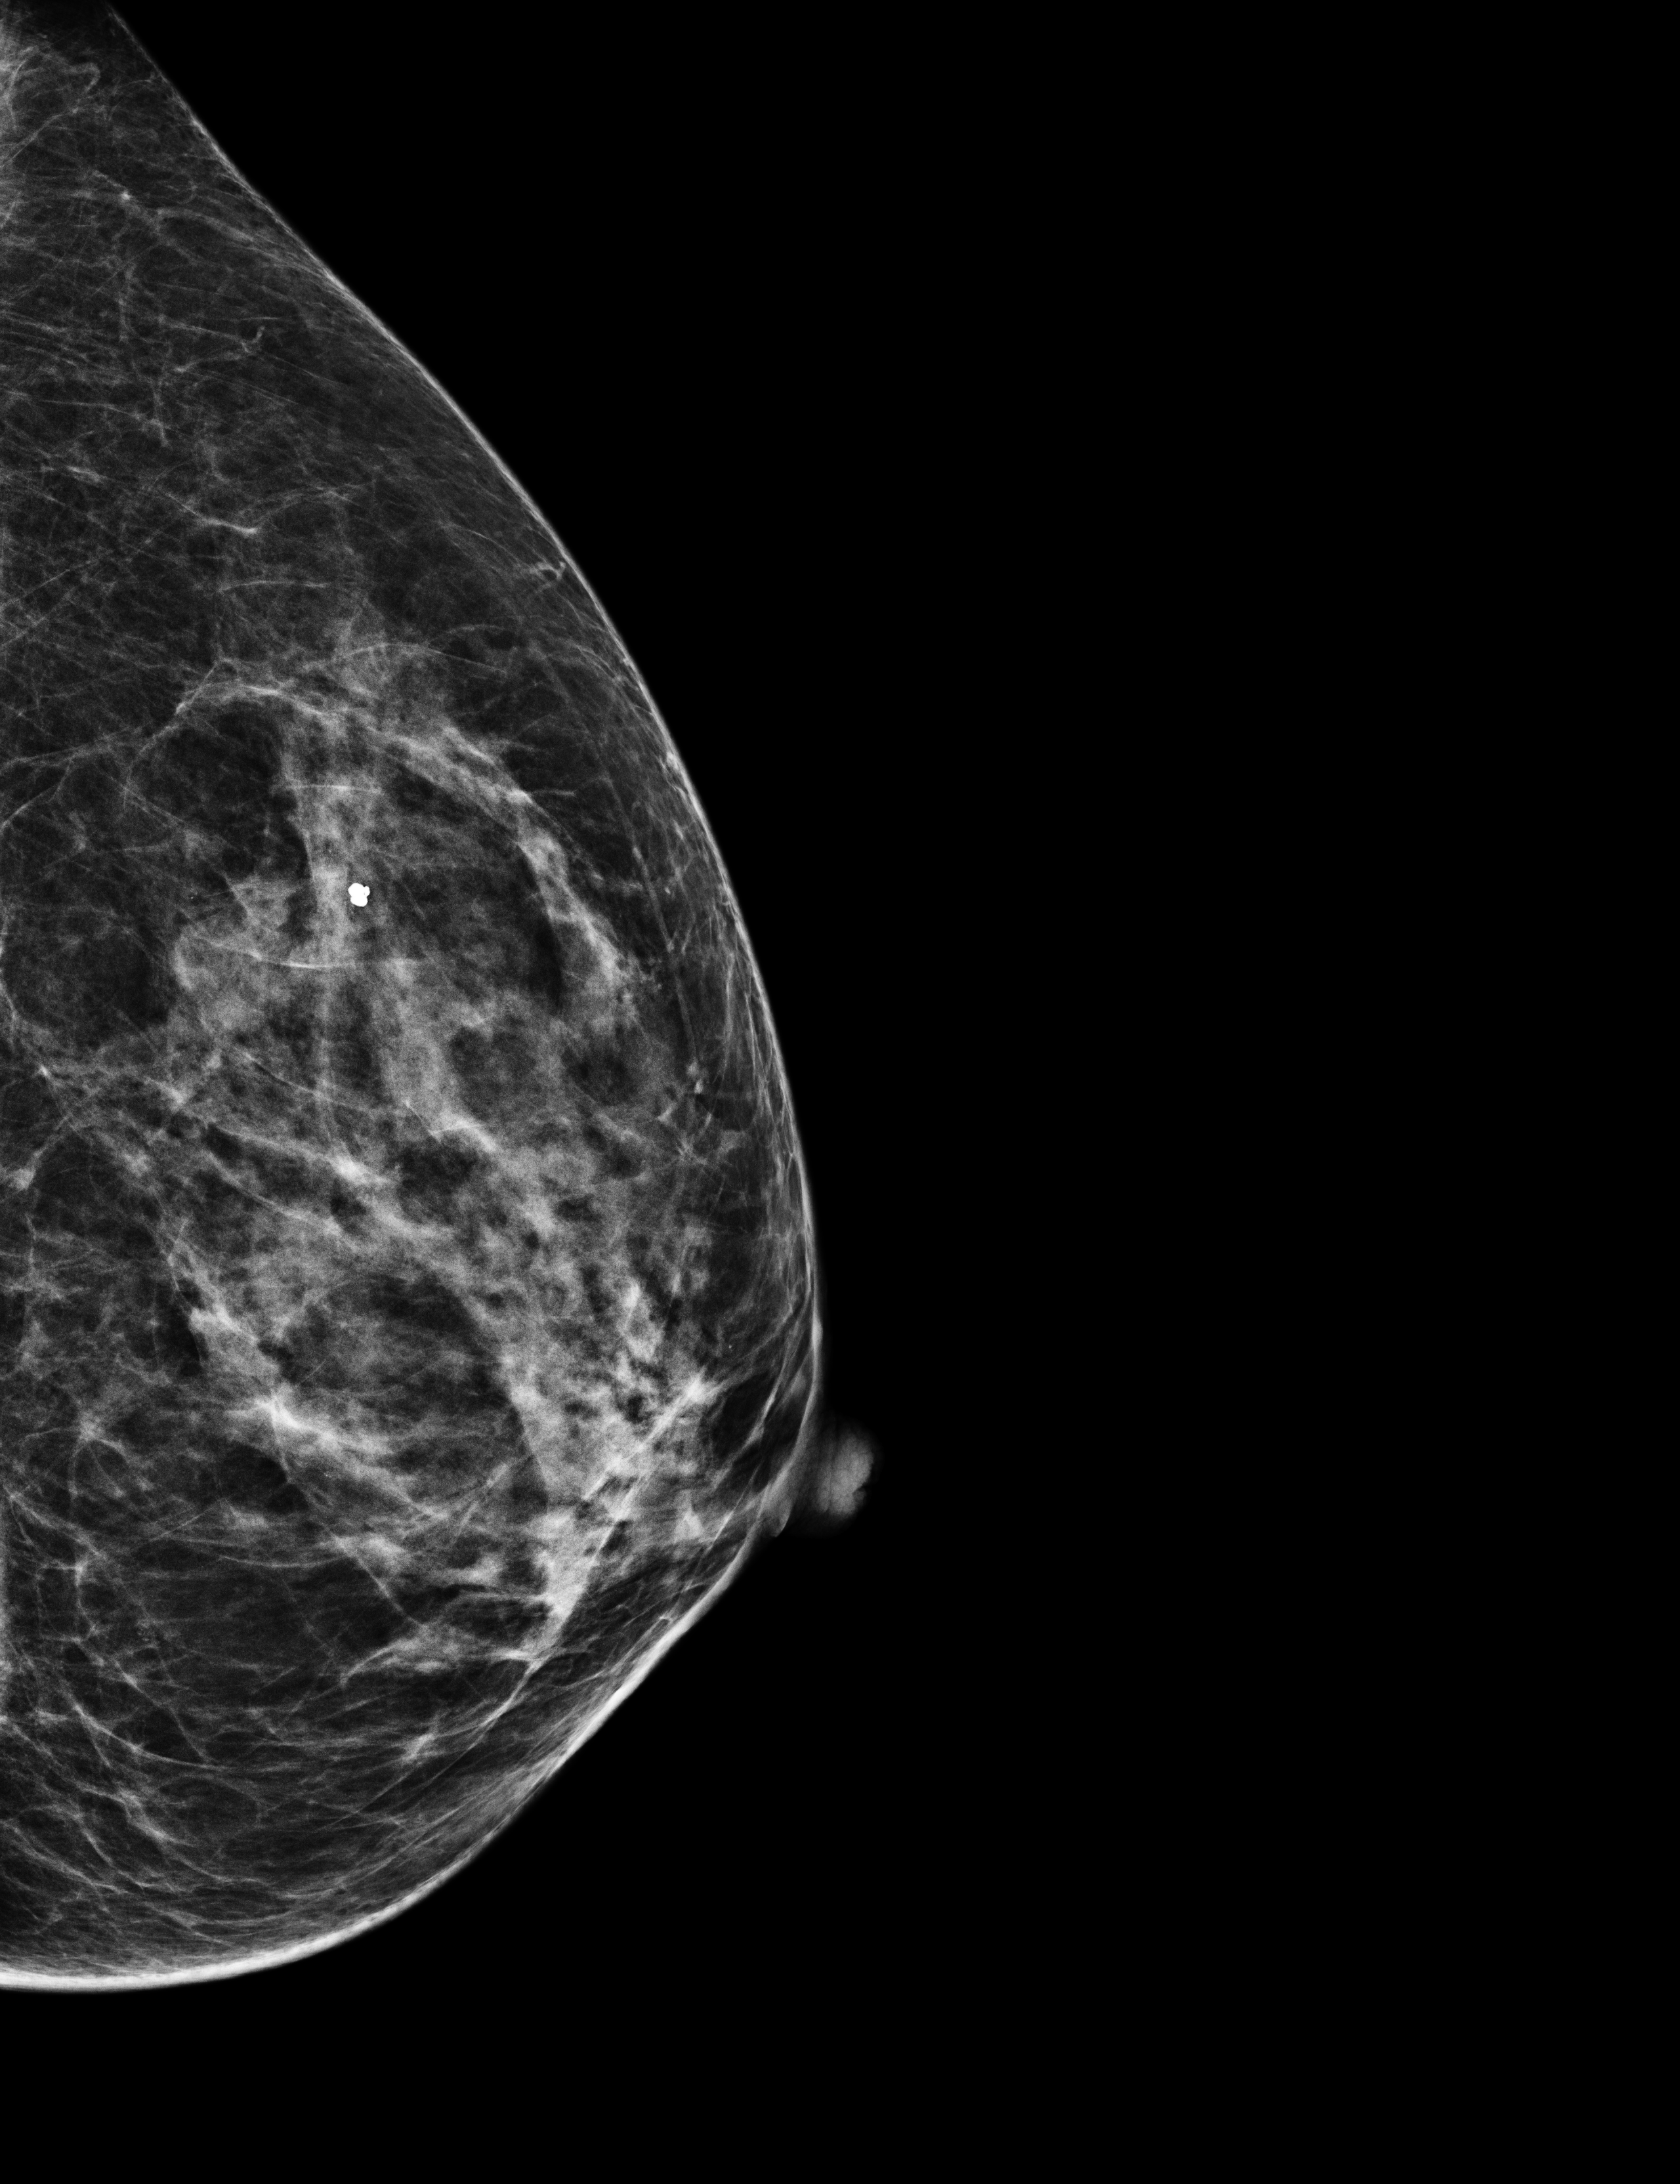
Digital mammogram (FFDM); left breast; laterally exaggerated craniocaudal (XCCL) view; annual screening mammography examination. Female patient, age 60 years.
Breast density at the screening exam (both breasts): heterogeneously dense (BI-RADS density category c). Final BI-RADS category for the screening round (tomosynthesis exam, both breasts): category 1. Recall: recalled for additional imaging after this screen.